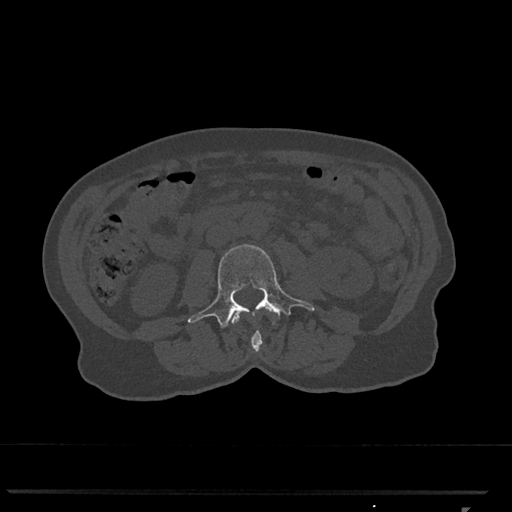
CT including the spine, one axial slice; slice 285 of 793 in the series (ordered by position); reconstruction kernel Br40s/3; bone window (W 1800 / L 400 HU); 0.5 mm slice thickness; 512 × 512 image matrix, field of view 380 × 380 mm. Female patient, age 62 years. Case-level facts recorded for this patient, not image findings: primary cancer: renal.
Outlined on this slice (semi-automatic segmentation, software-assisted and operator-edited):
- L2 vertebra: box from (x=231, y=308) to (x=272, y=352) px
- L3 vertebra: (x=187, y=244)–(x=315, y=327)